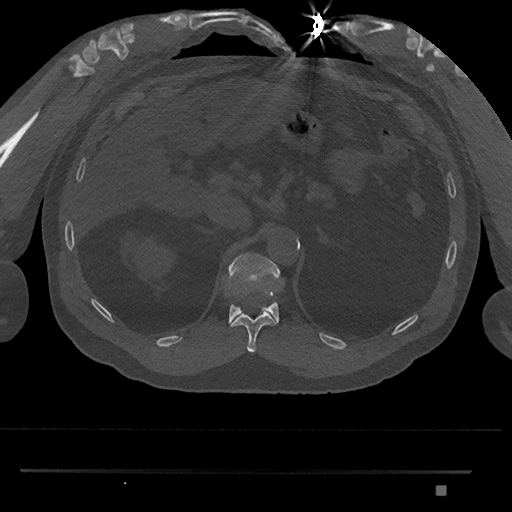
CT including the spine, one axial slice; position 921 of 1134 along the scan axis; bone window (W 1800 / L 400 HU); 0.5 mm slice thickness; 512 × 512 image matrix. Patient: male, 65 years. Case-level facts recorded for this patient, not image findings: primary cancer: prostate.
Structures marked on this image (semi-automatic segmentation, software-assisted and operator-edited):
- T11 vertebra: box from (x=230, y=311) to (x=277, y=353) px
- T12 vertebra: (x=225, y=252)–(x=280, y=324)